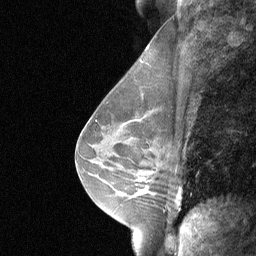
Breast MRI (dynamic contrast-enhanced), one sagittal slice. Slice 40 of 64 in the series (ordered by position). Dynamic contrast-enhanced study with each time point stored as its own series, time point 2 of 3 at this slice position (early post-contrast, ordered by acquisition time). 1.5 T. TE 4.8 ms, TR 27 ms. 2 mm slice thickness. 256 × 256 image matrix. Female patient, age 48 years. From the clinical record (not read from this slice): setting: breast cancer imaged before/during neoadjuvant chemotherapy; receptor status: HR-positive, HER2-negative.
Outlined on this slice (semi-automatic segmentation, software-assisted and operator-edited):
- analysis volume of interest (the breast-tissue region the enhancement analysis was run in; not a lesion): box from (x=131, y=165) to (x=159, y=198) px
- tumour enhancement mask (voxels above the 90 % enhancement threshold inside the analysis volume of interest): (x=144, y=190)–(x=147, y=192)